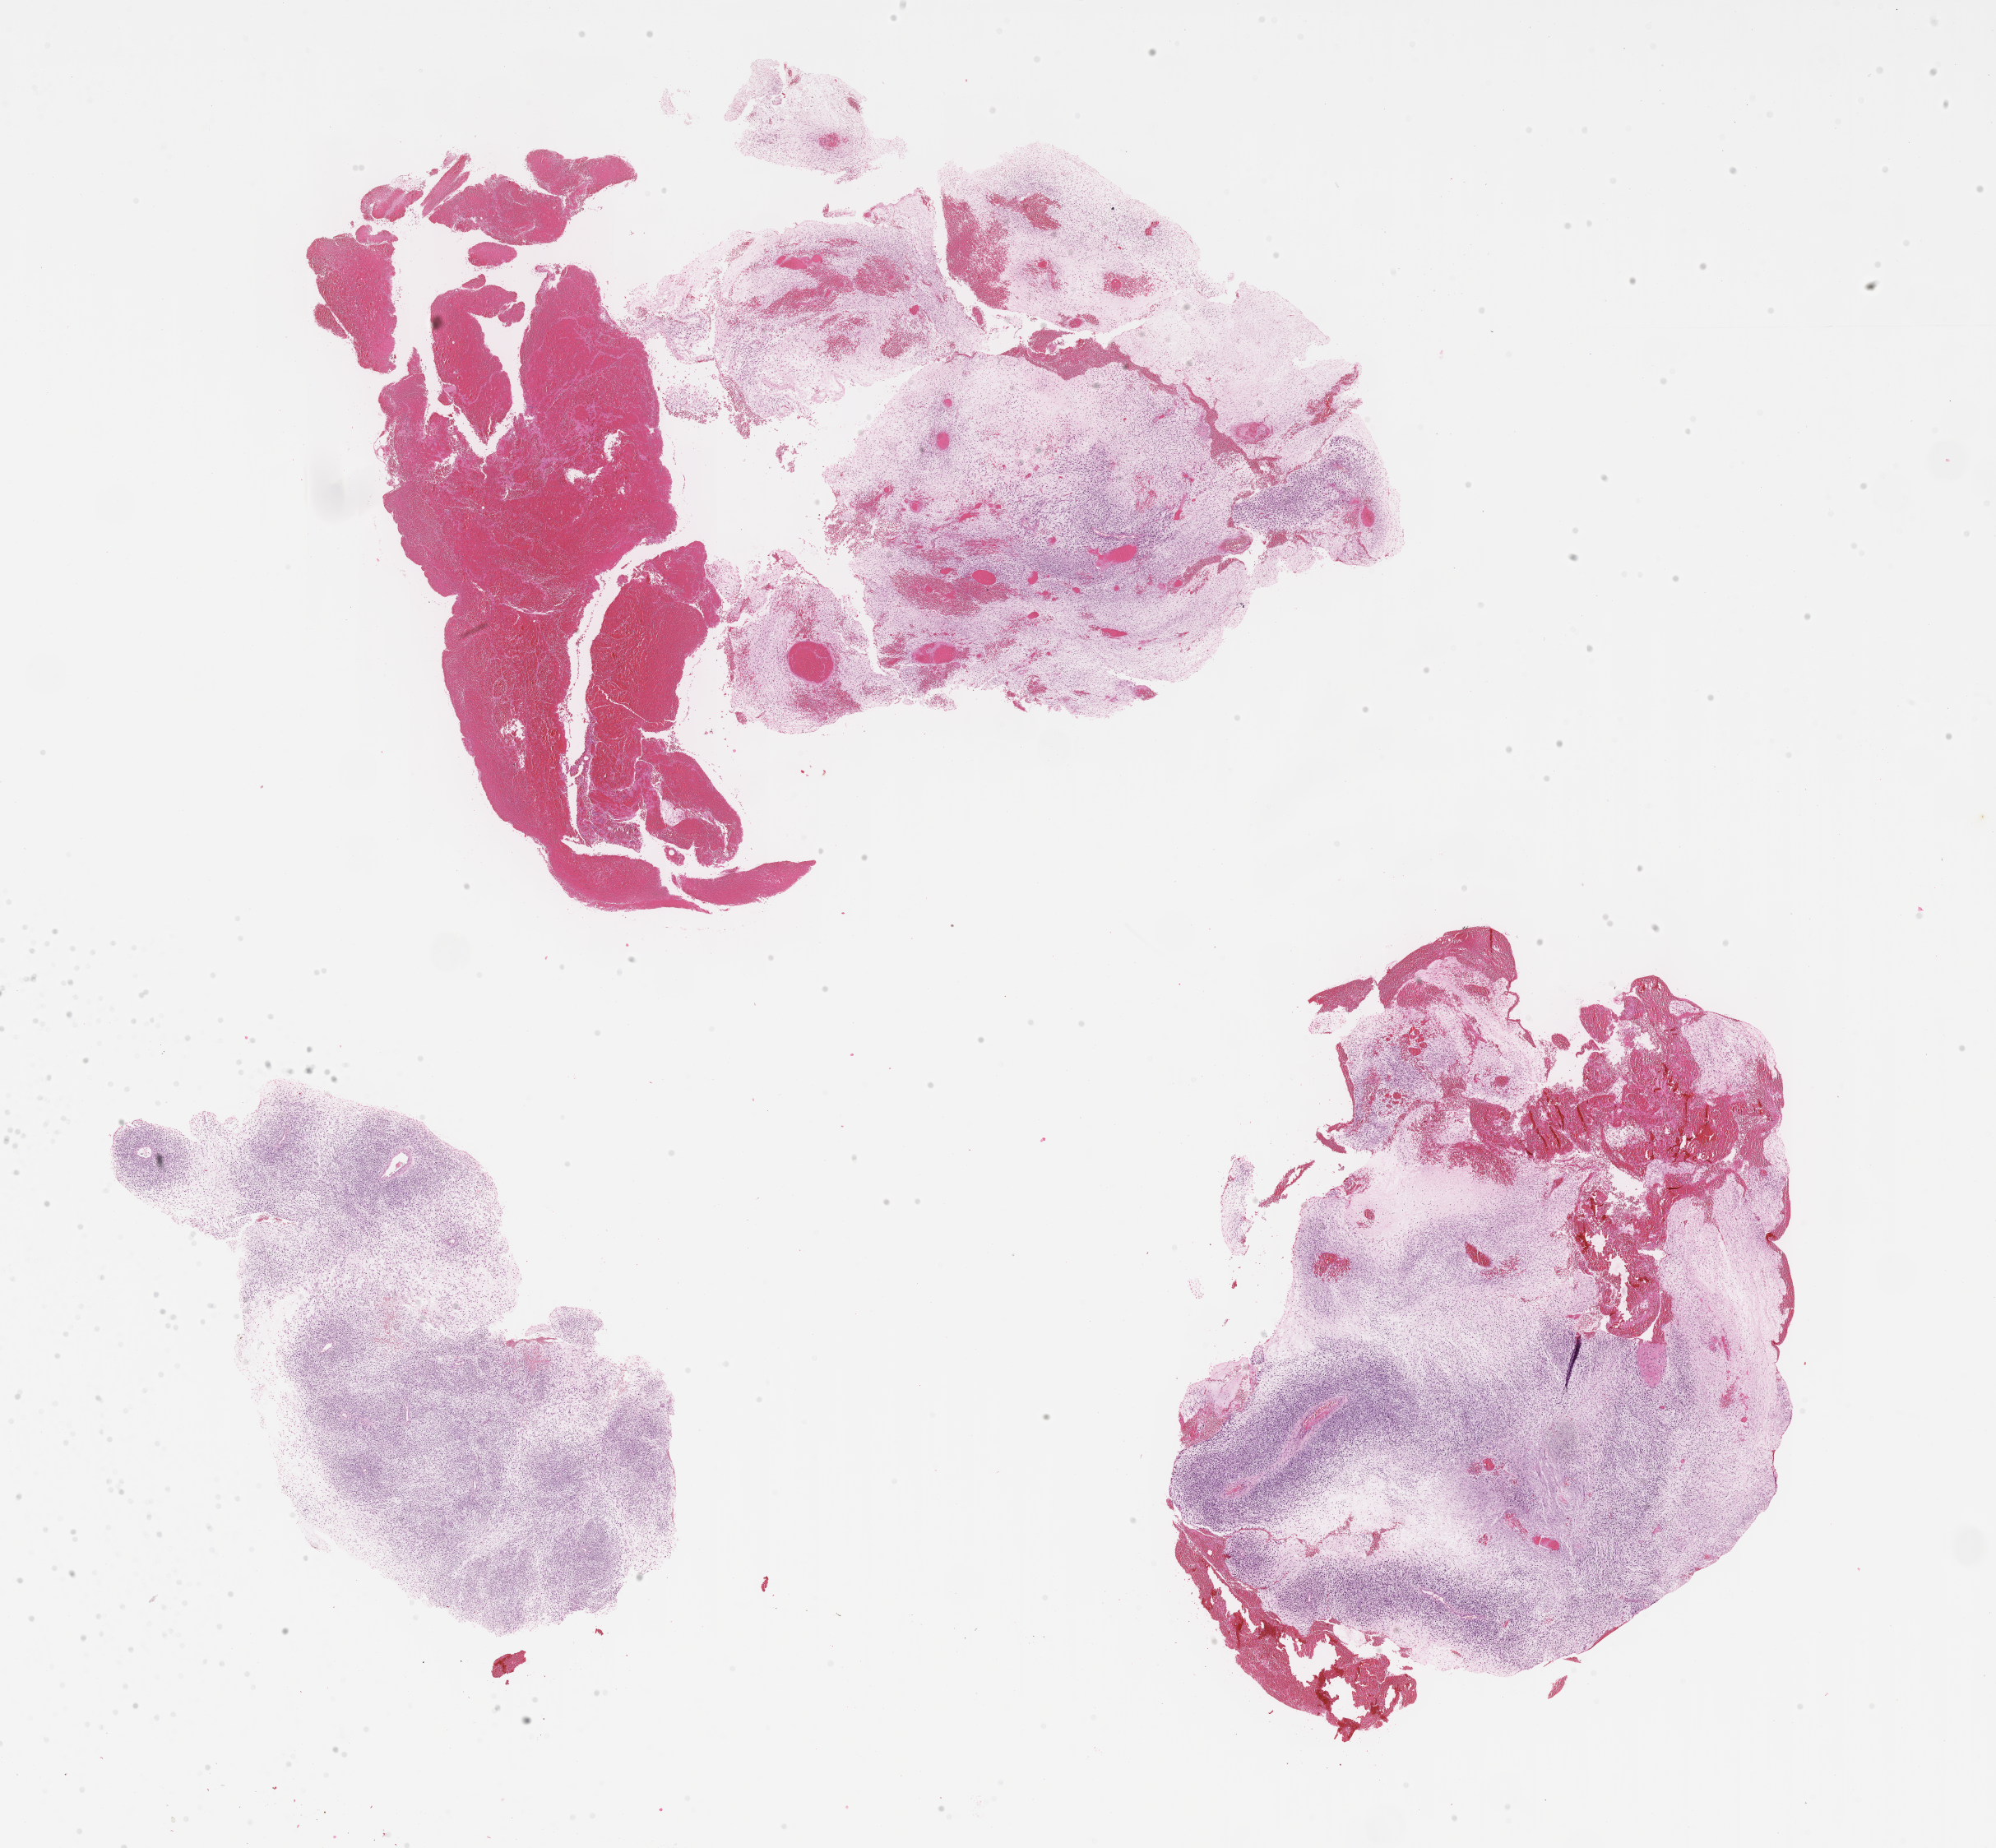
Digitized hematoxylin and eosin (H&E)-stained section of tumor tissue, low-resolution overview of the scanned area, about 19.6 x 18.2 mm, FFPE section, site: soft tissue, abdomen. Patient: male, age 3.3 years at diagnosis.
• stage (as recorded): 4
• diagnosis: rhabdomyosarcoma; histological classification: embryonal rhabdomyosarcoma
• metastatic status at presentation (as recorded): metastatic
• primary site (case record): retroperitoneum